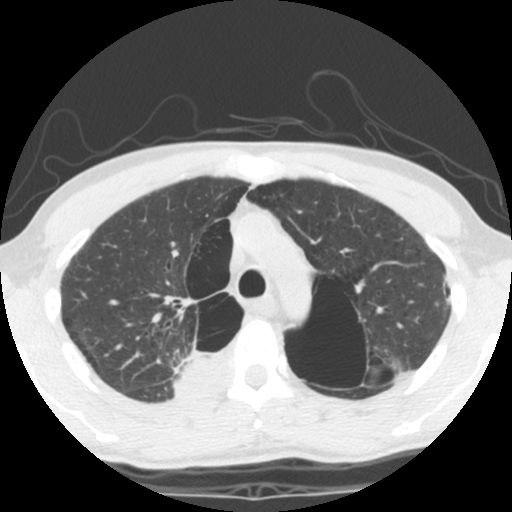
Low-dose screening chest CT, one axial slice; position 86 of 119 along the scan axis; 140 kVp; lung window (W 1500 / L -600 HU); 512 × 512 image matrix.
Structures marked on this image (outlined manually by an expert reader):
- lesion 1 (tumor, upper lobe of right lung): bounding box (x1, y1, x2, y2) in pixels: (175, 352, 234, 397)